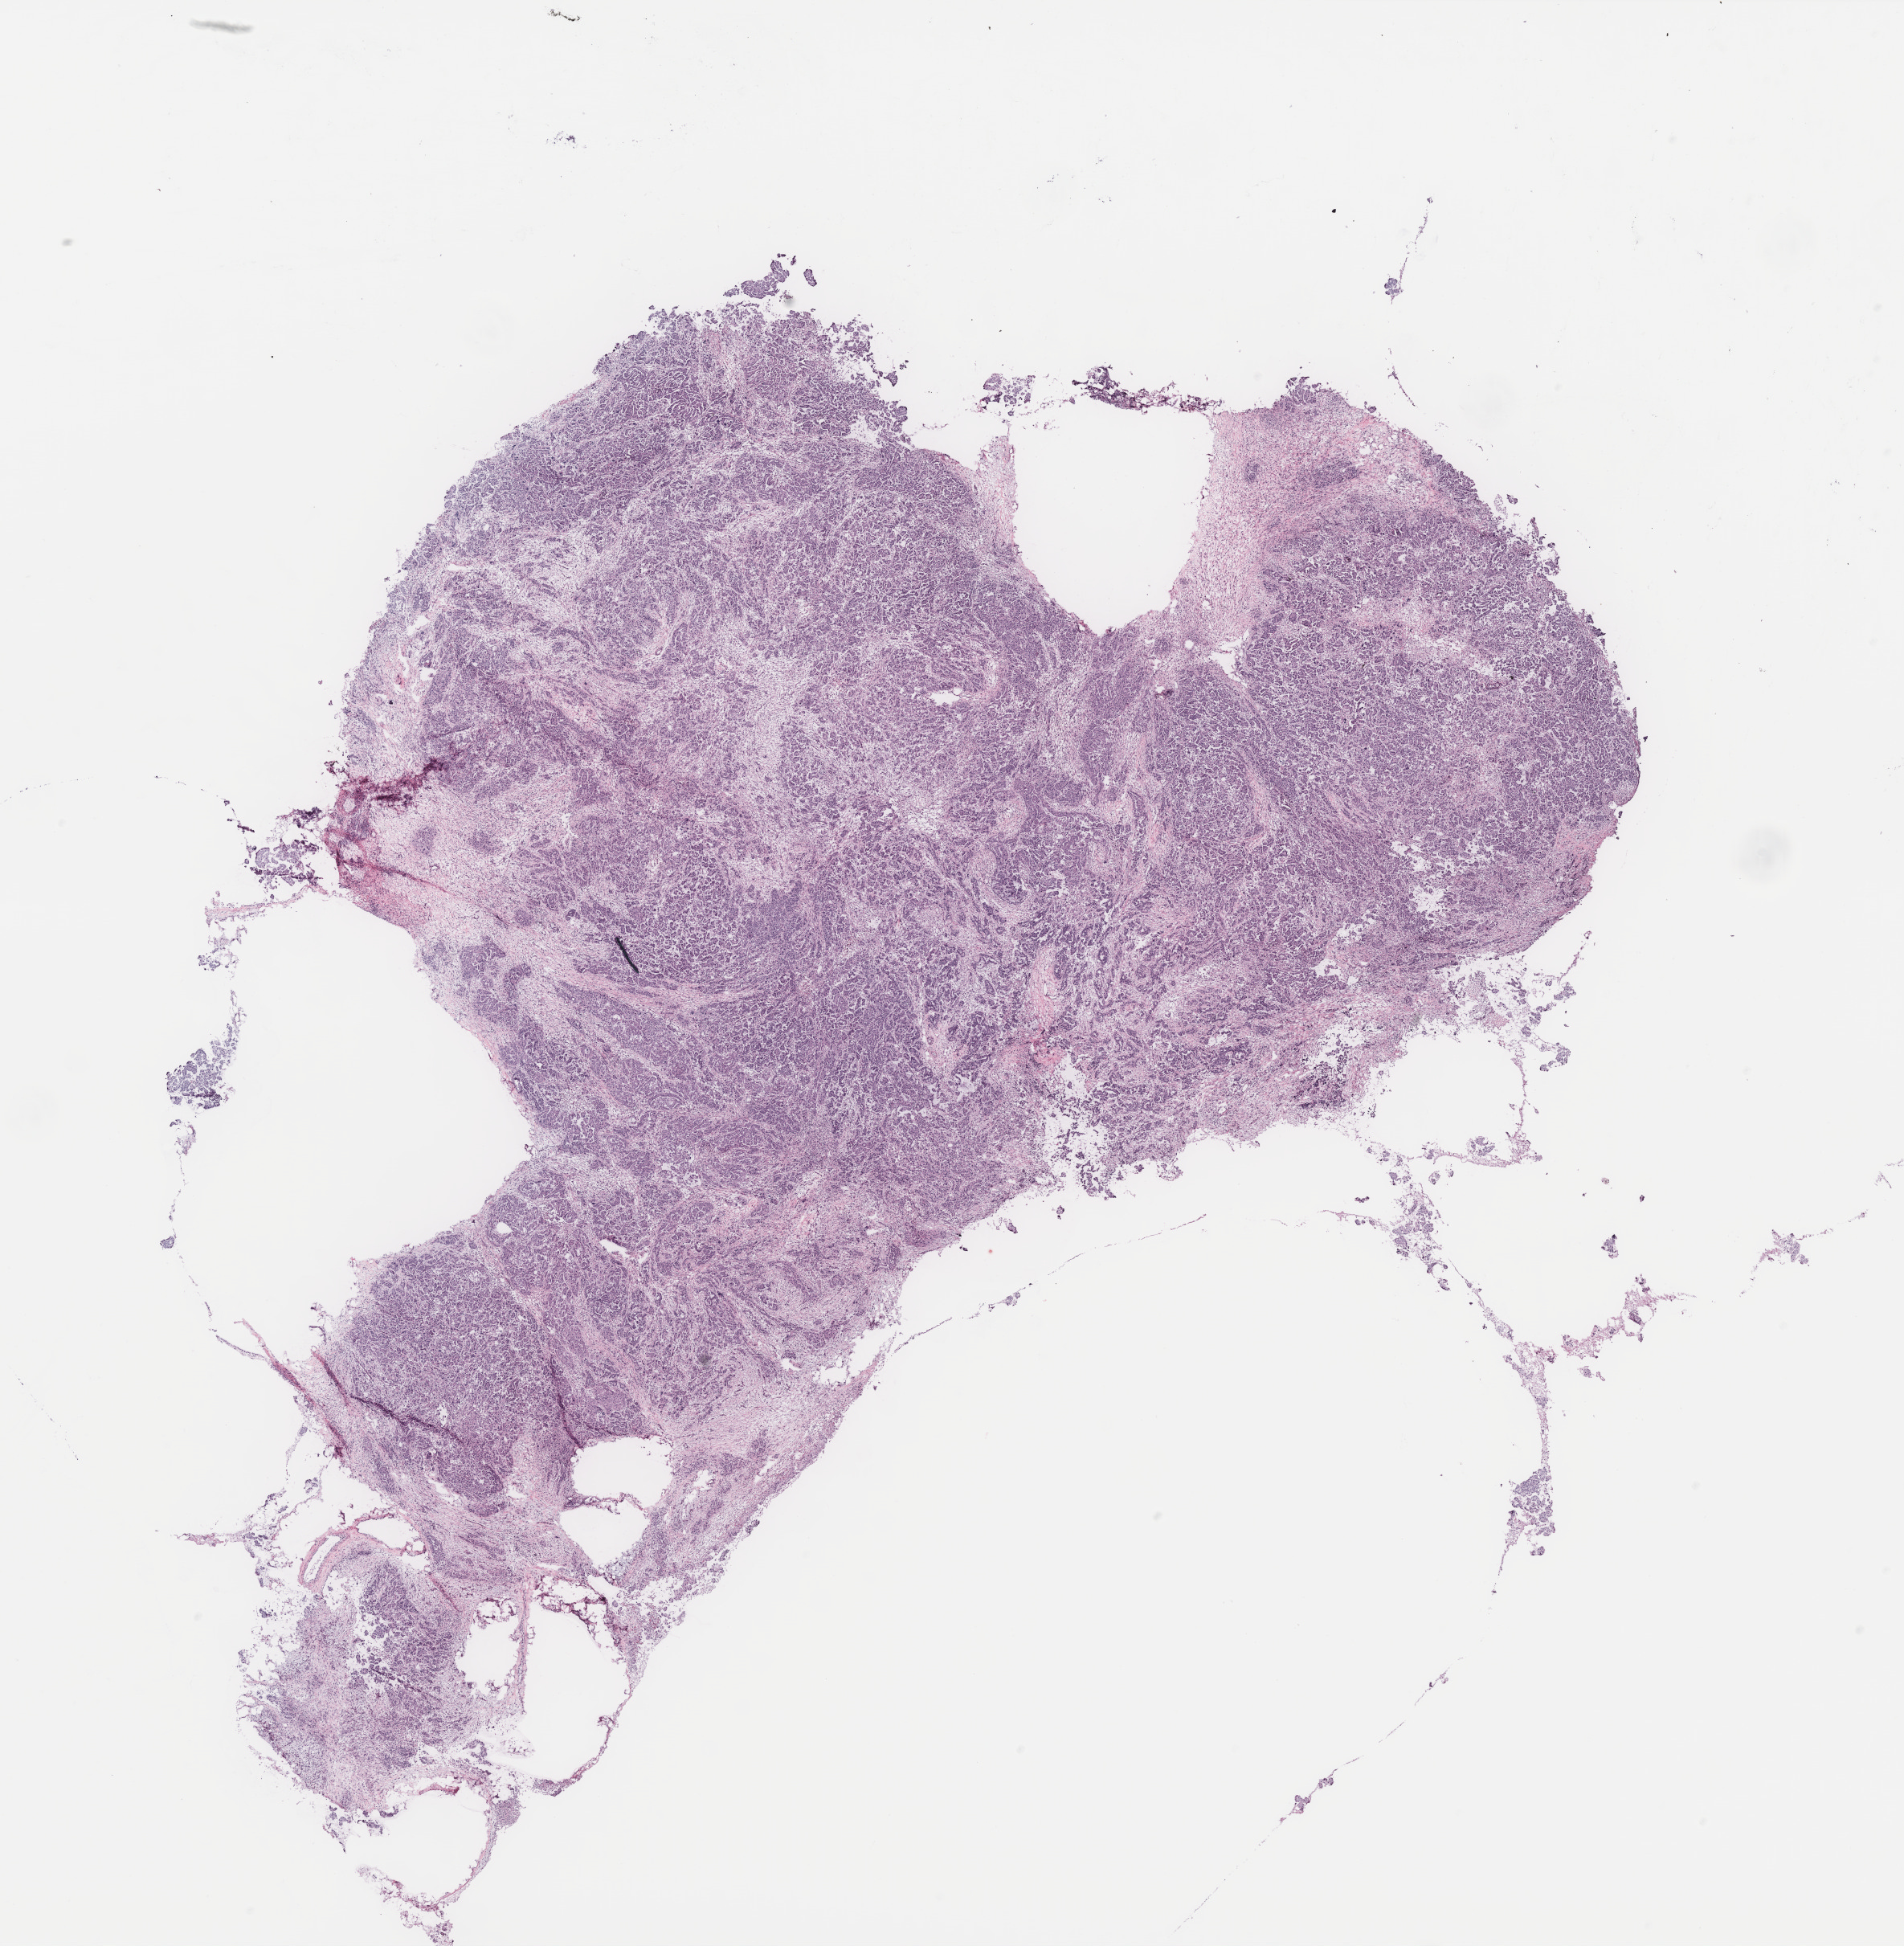
Whole-slide histology image, H&E-stained — a low-resolution overview of the entire scanned area, about 19.0 x 19.4 mm, tumour tissue sample, ovary. 59-year-old female patient.
Diagnosis: Serous adenocarcinoma, NOS.